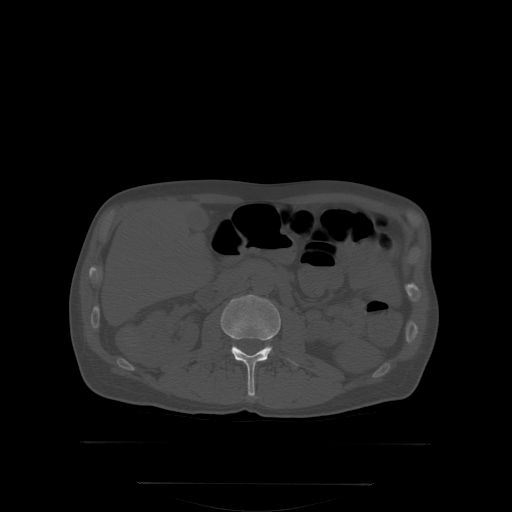
CT including the spine, one axial slice. Slice 136 of 350 in the series (ordered by position). Bone window (W 1800 / L 400 HU). 512 × 512 image matrix, field of view 500 × 500 mm. Patient: male, 58 years. From the clinical record (not read from this slice): primary cancer: prostate.
Outlined on this slice (semi-automatically segmented with operator editing):
- L2 vertebra: bounding box (x1, y1, x2, y2) in pixels: (197, 296, 298, 399)